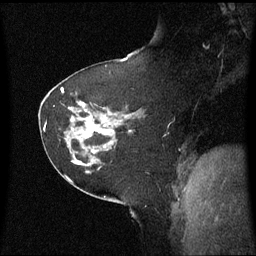
Breast MRI (dynamic contrast-enhanced), one sagittal slice; position 34 of 60 along the scan axis; dynamic contrast-enhanced series, image 2 of 3 at this slice position (ordered by acquisition); 1.5 T; TE 4.2 ms, TR 8.4 ms; 256 × 256 image matrix, field of view 220 × 220 mm. Patient: female, 60 years. Case-level facts recorded for this patient, not image findings: setting: breast cancer imaged before/during neoadjuvant chemotherapy; receptor status: triple-negative.
Outlined on this slice (semi-automatic segmentation, software-assisted and operator-edited):
- analysis volume of interest (the breast-tissue region the enhancement analysis was run in; not a lesion): bounding box [x1, y1, x2, y2] px = [64, 102, 128, 161]
- tumour enhancement mask (voxels above the 70 % enhancement threshold inside the analysis volume of interest): [89, 122, 97, 133]